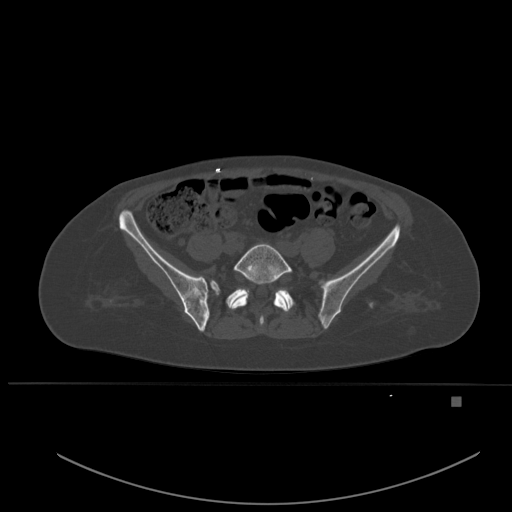
CT including the spine, one axial slice; slice 149 of 651 in the series (ordered by position); bone window (W 1800 / L 400 HU); 512 × 512 image matrix, field of view 443 × 443 mm. Patient: female, 49 years. From the clinical record (not read from this slice): primary cancer: breast.
Structures marked on this image (semi-automatic segmentation, software-assisted and operator-edited):
- L5 vertebra: bounding box [x1, y1, x2, y2] px = [230, 244, 292, 326]